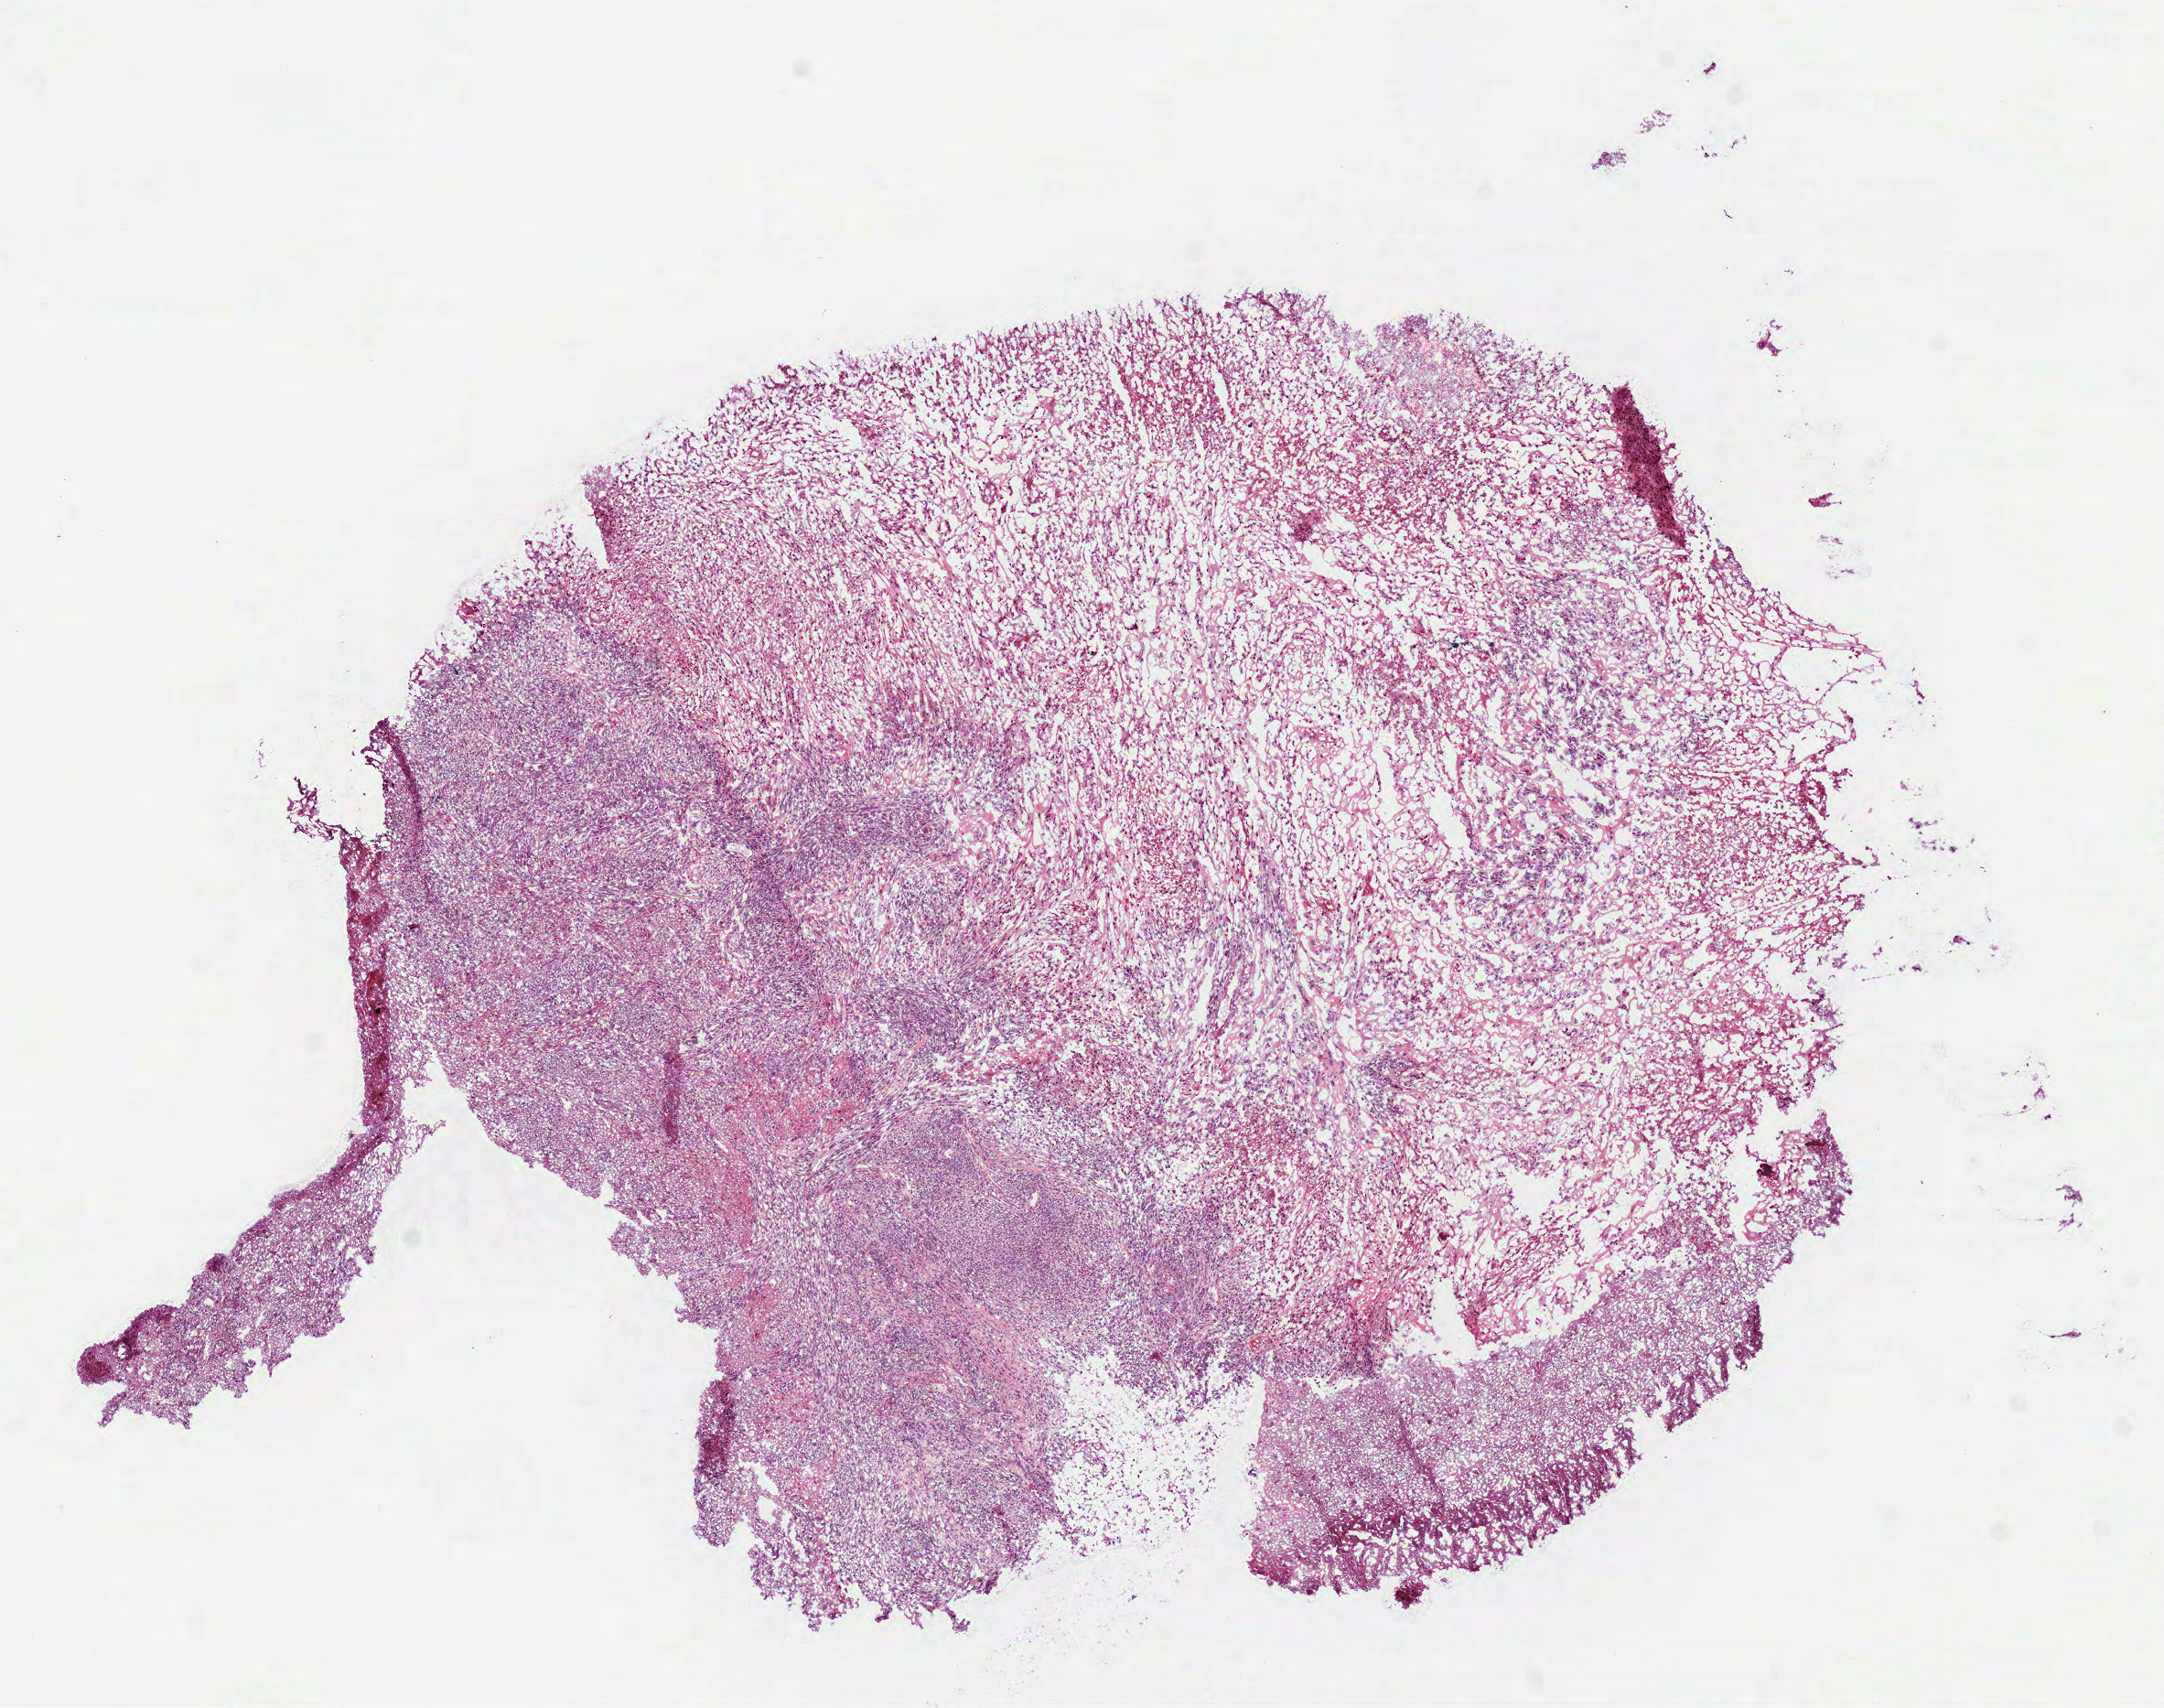
Digitized H&E tissue section (whole slide), a low-resolution overview of the entire scanned area, about 9.5 x 7.5 mm, frozen section from the bottom of the tissue portion, recurrent tumour sample from the brain. Male patient; age at initial diagnosis 36 years. Slide review estimates, as recorded: tumour cells 80%, tumour nuclei 80%, normal cells 0%, stromal cells 0%, necrosis 20%.
This section: recurrent tumour. Patient diagnosis: Glioblastoma.